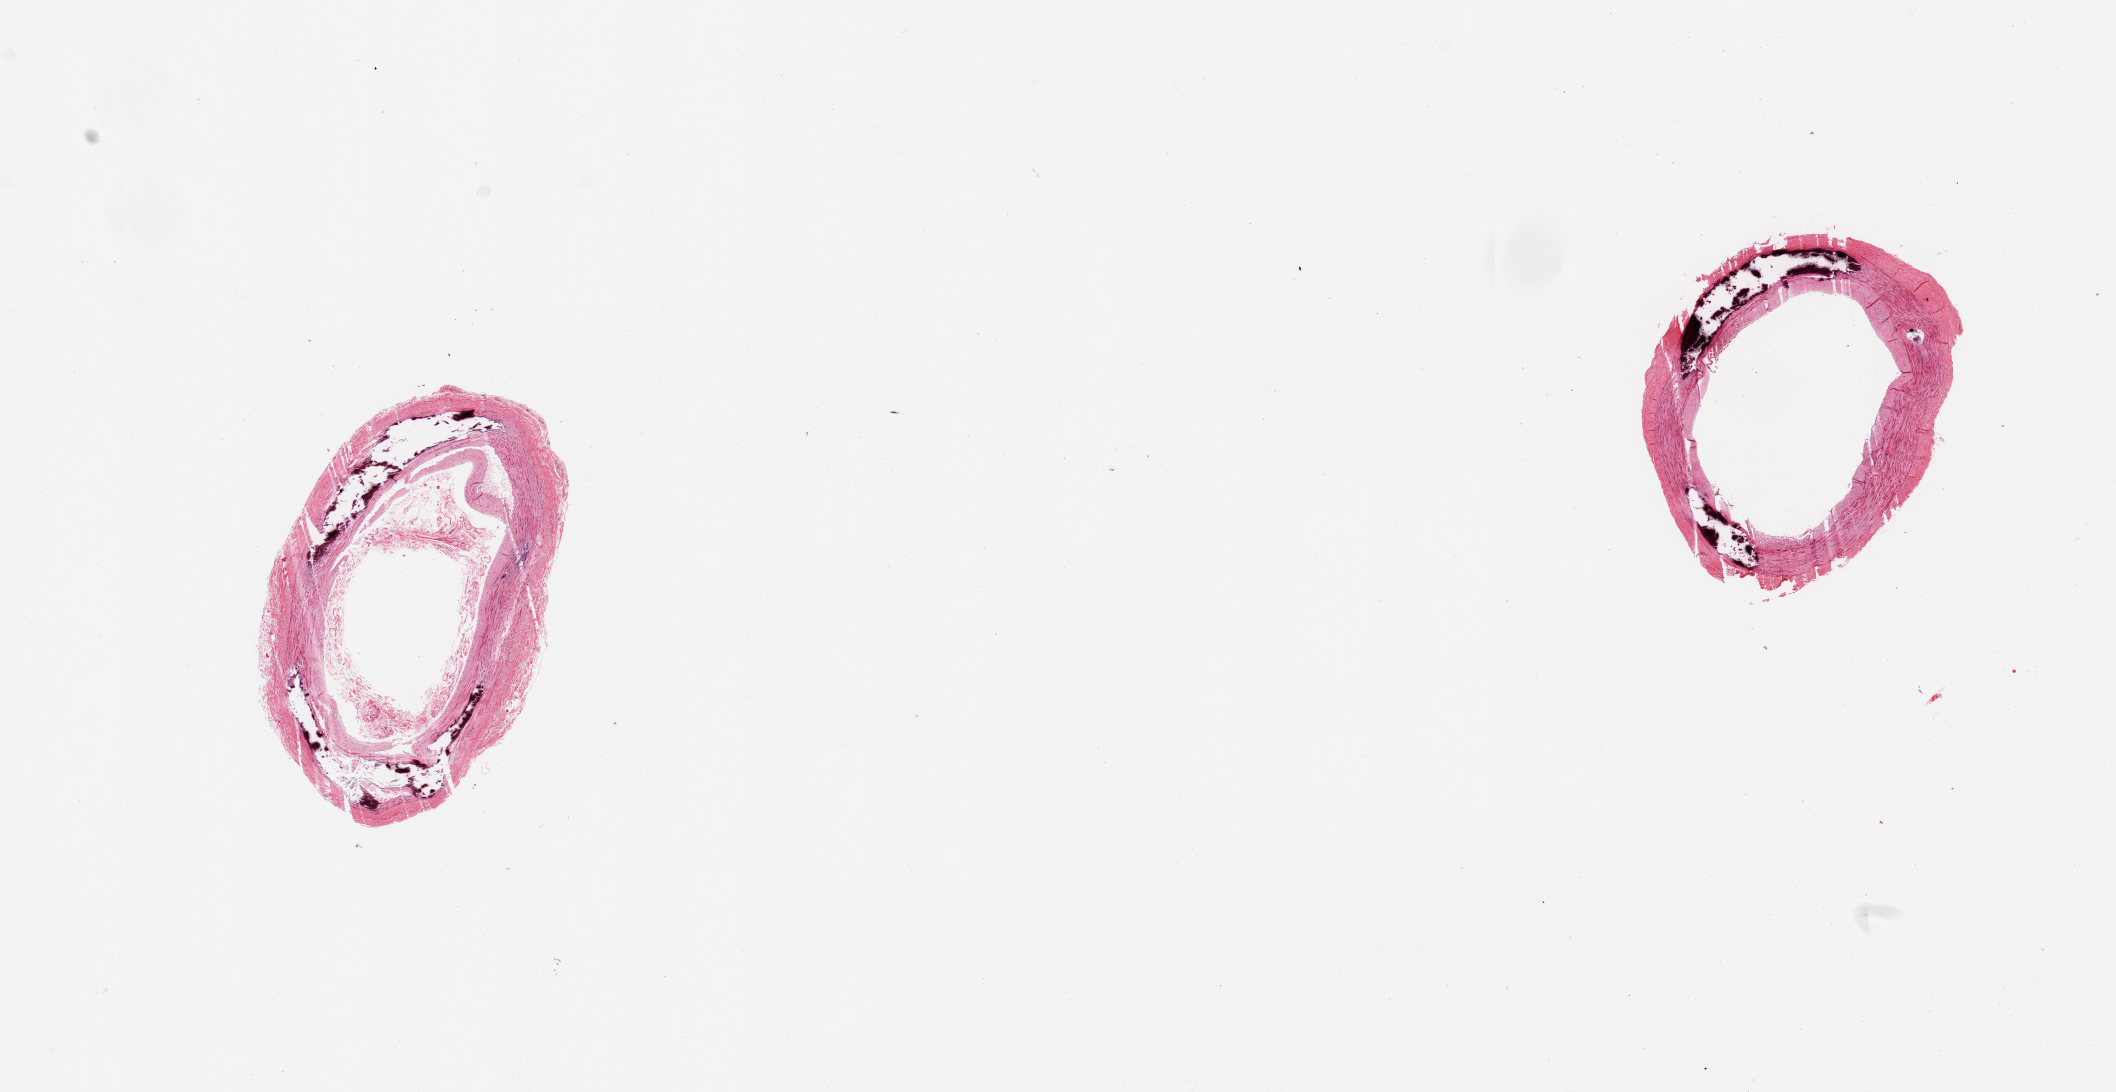
Whole-slide image, H&E stain, brightfield, shown as a low-resolution overview of the whole scanned area (about 16.7 x 8.6 mm, slide scanned at 20x). PAXgene-fixed, paraffin-embedded tissue. Section of tibial artery (target tissue). Donor tissue sample.
Reviewer comment on this tissue sample: 2 pieces, excellent clean specimens; no atherosis; foci of Monckeberg's medial sclerosis.